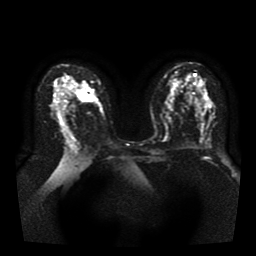
Breast MRI, one axial slice; slice 23 of 41 in the series (ordered by position); diffusion-weighted series; image 2 of 4 stored at this slice position (different b-values; order by instance number); 1.5 T; 5 mm slice thickness; 256 × 256 image matrix, field of view 330 × 330 mm. Female patient.
Structures marked on this image (expert manual segmentation):
- tumour on diffusion-weighted imaging: bounding box [x1, y1, x2, y2] px = [79, 83, 94, 102]